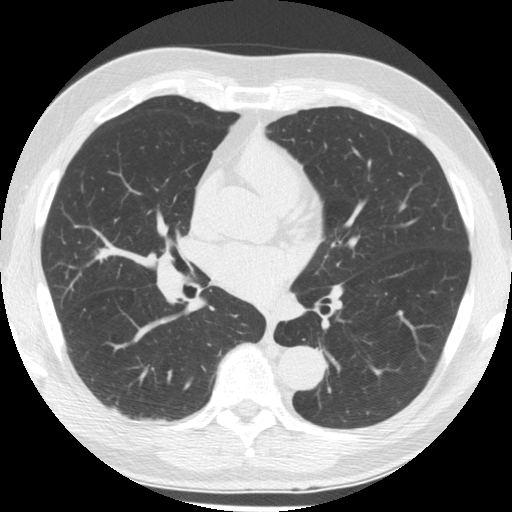
Low-dose screening chest CT, one axial slice. Position 96 of 176 along the scan axis. 120 kVp. Lung window (W 1500 / L -600 HU). 2.5 mm slice thickness. 512 × 512 image matrix.
Outlined on this slice (outlined manually by an expert reader):
- lesion 1 (tumor, middle lobe of right lung): box from (x=94, y=248) to (x=113, y=263) px